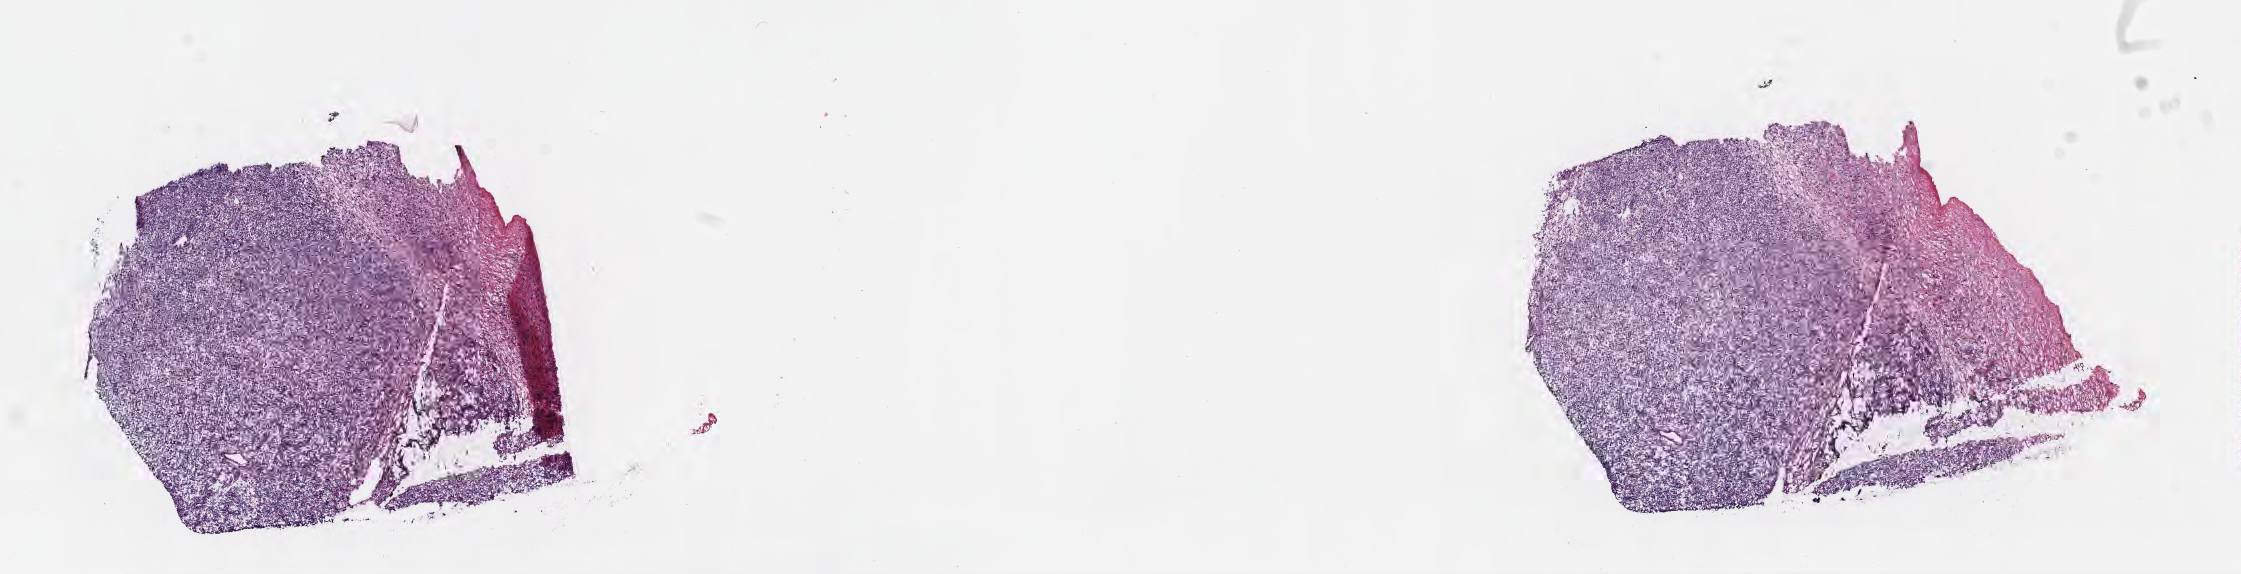
Digitized hematoxylin and eosin (H&E)-stained section, a low-resolution overview of the entire scanned area, about 18.1 x 4.6 mm; frozen section (tissue freezing medium); specimen: recurrent tumor; anatomic site: testis. Male patient; age at initial diagnosis 8 years. Pathologist review of this section (percent, as recorded): tumor cells 80%, tumor nuclei 90%, stromal cells 15%, necrosis 5%, normal cells 0%. Inflammatory infiltration, as recorded: lymphocyte infiltration 50%, monocyte infiltration 20%, neutrophil infiltration 0%.
- section: top of the tissue portion
- patient diagnosis: Burkitt lymphoma, NOS